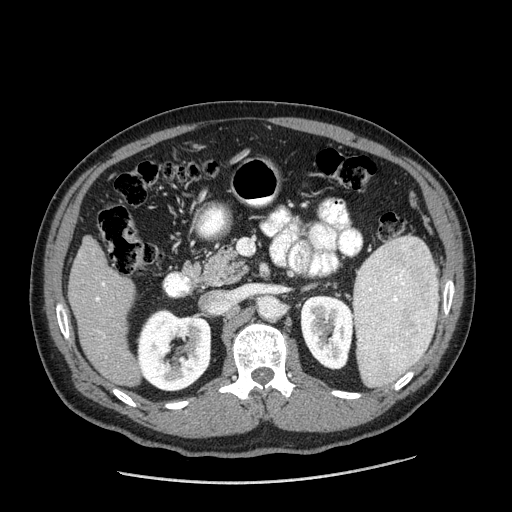
Contrast-enhanced abdominal CT (liver protocol), one axial slice; slice 75 of 198 in the series (ordered by position); one of 2 acquisitions stored at this slice position; soft-tissue window (W 400 / L 40 HU); 2.5 mm slice thickness; 512 × 512 image matrix, field of view 400 × 400 mm. From the clinical record (not read from this slice): diagnosis: hepatocellular carcinoma (patient treated with transarterial chemoembolisation; whether this scan precedes or follows treatment is not stated here); TNM stage (as recorded): Stage-II; Child-Pugh class: A.
Annotated regions visible in this slice (semi-automatically segmented with operator editing):
- liver parenchyma outside the tumour (the mass and vessels are separate outlines, so this box may not span the whole liver): bounding box (x1, y1, x2, y2) in pixels: (68, 236, 140, 386)
- liver vessels: (96, 283, 105, 337)